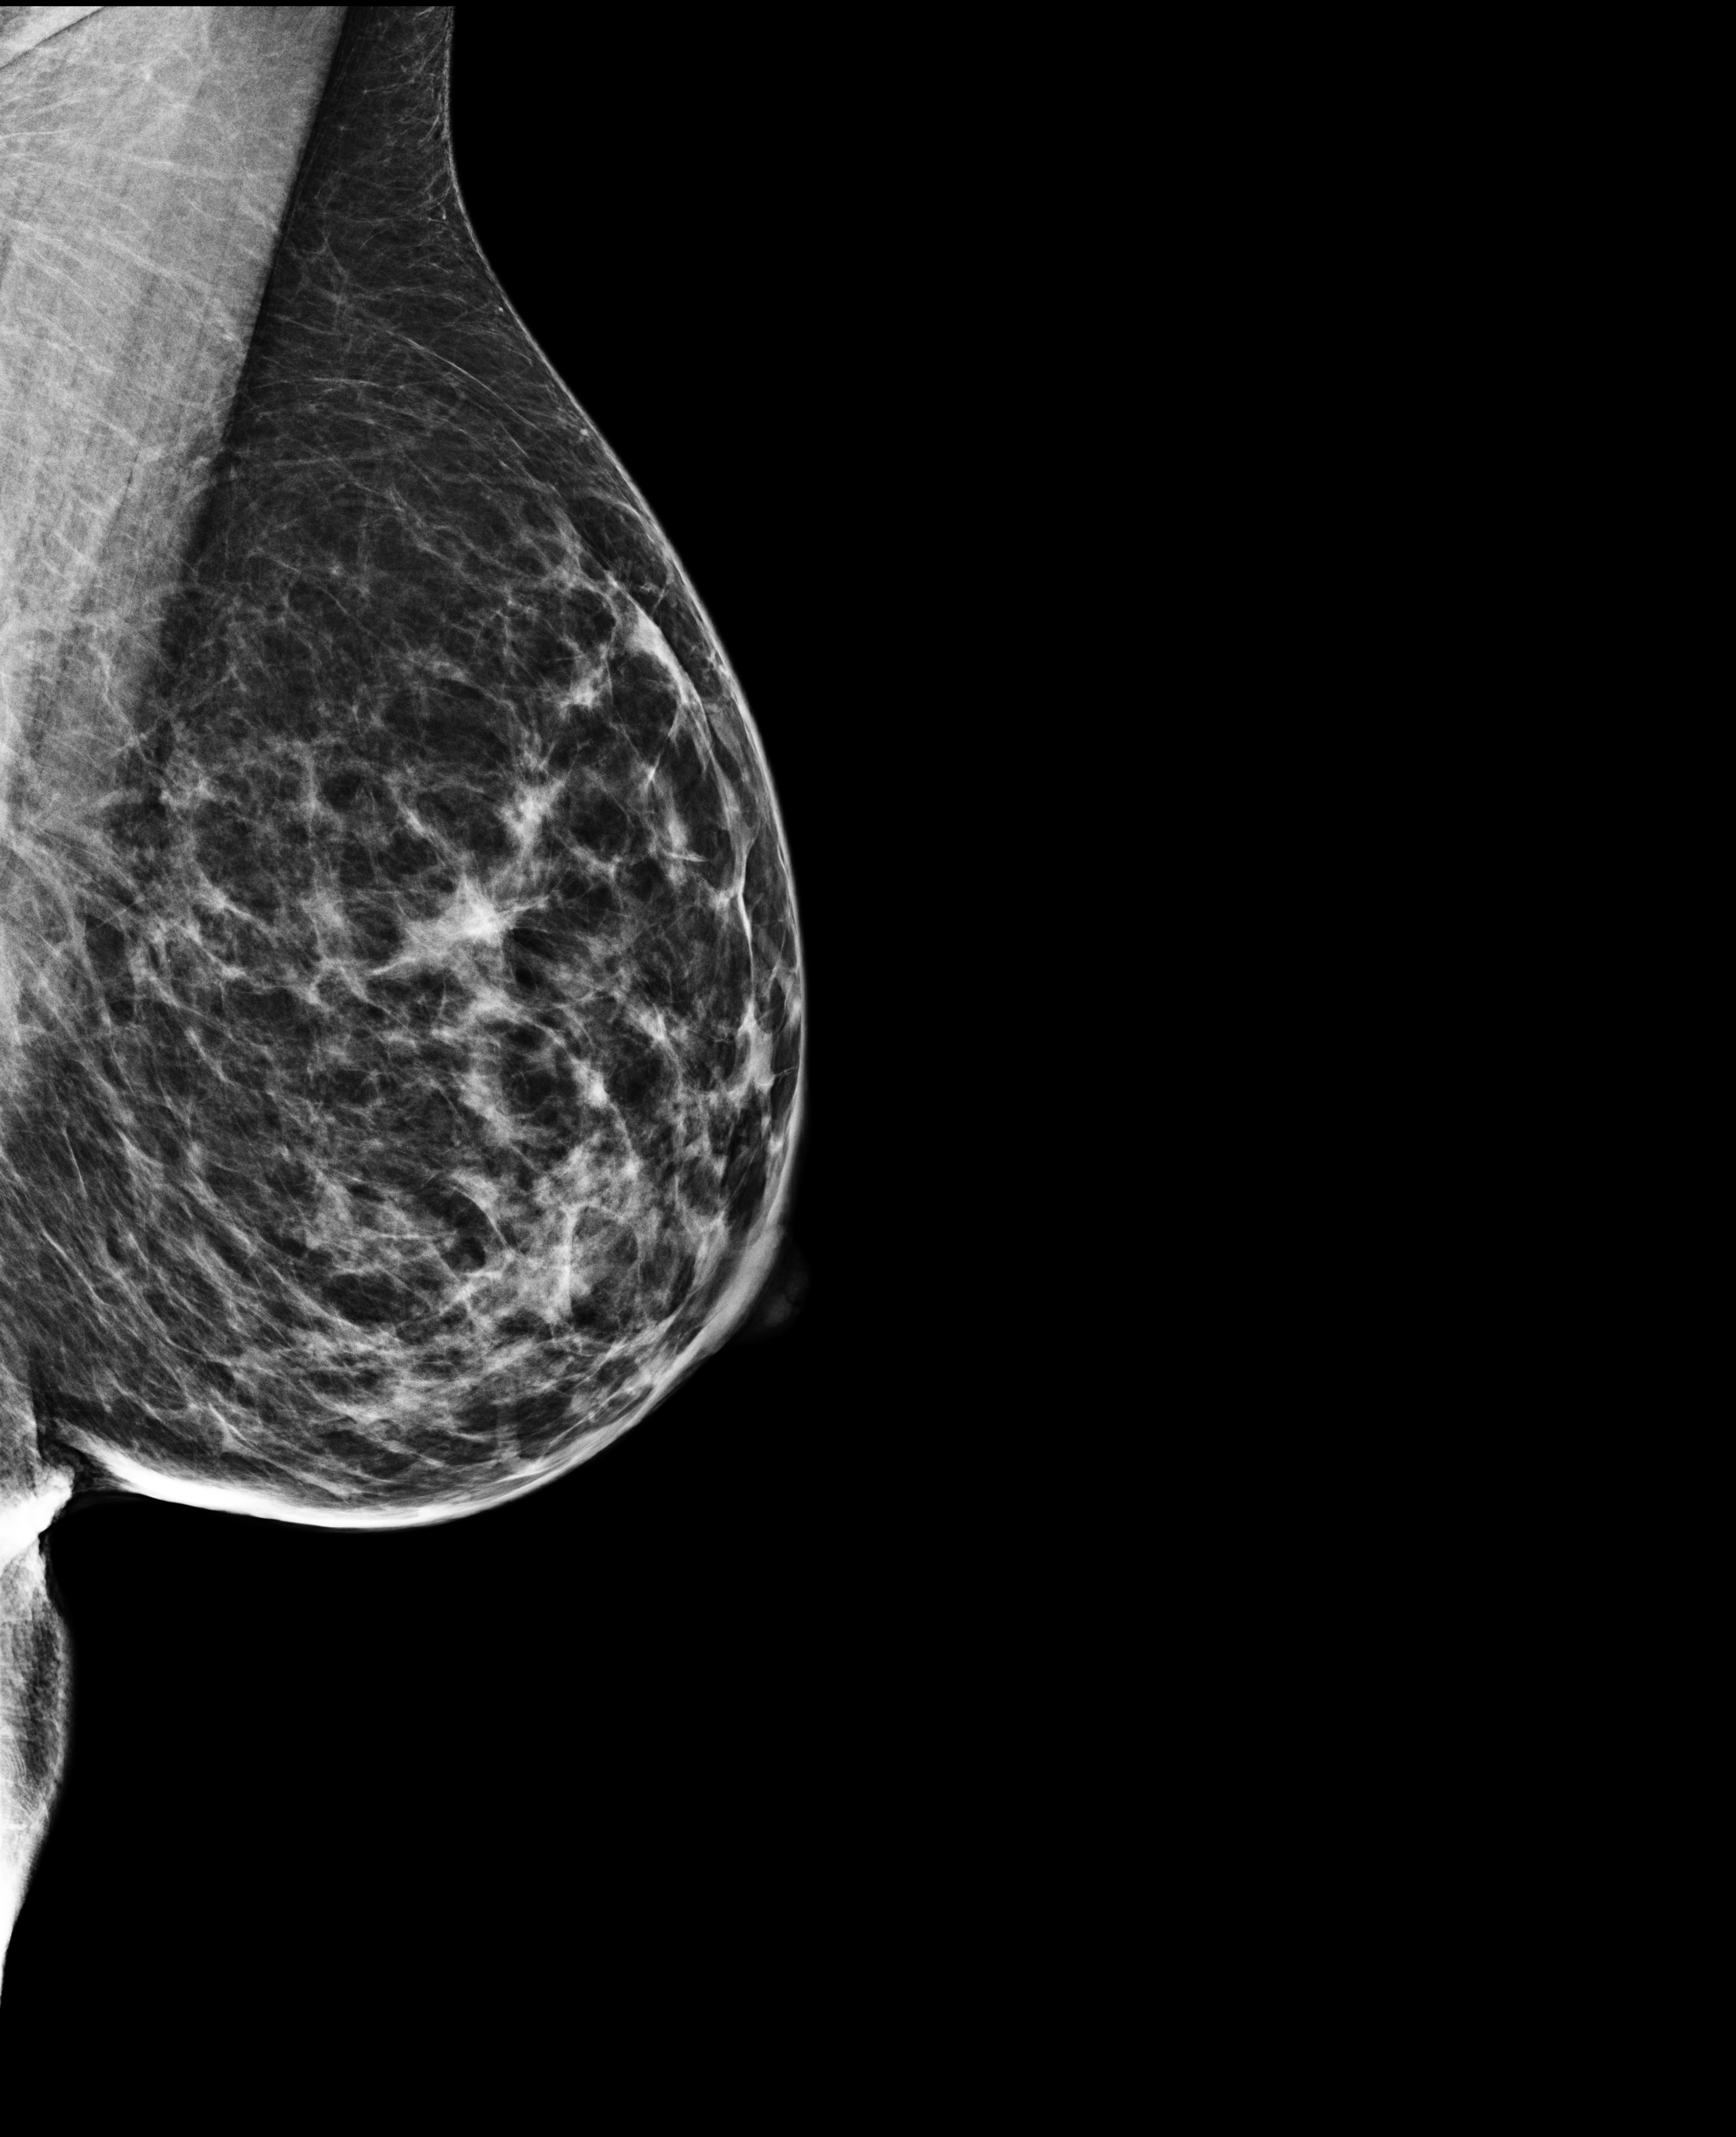
Annual screening mammography examination; system: Selenia Dimensions. Patient aged 49 years (female).
Image type: full-field digital mammogram. Breast: left. Projection: MLO view.